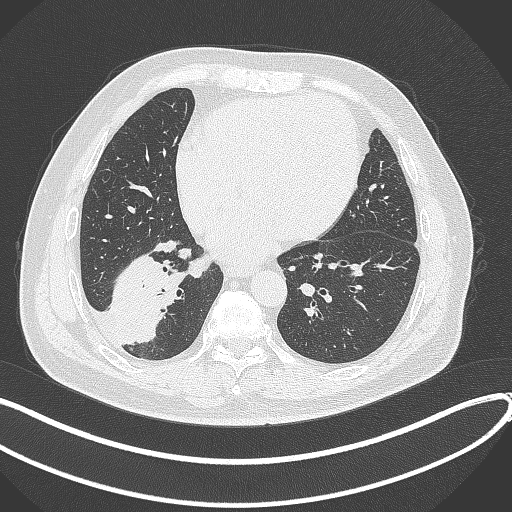
Chest CT, one axial slice. Position 129 of 360 along the scan axis. Lung window (W 1500 / L -600 HU). 1 mm slice thickness. 512 × 512 image matrix. Male patient, age 59 years.
Structures marked on this image (rectangle marked by the reading radiologist):
- lung tumour (recorded histology: adenocarcinoma): bounding box [x1, y1, x2, y2] px = [105, 248, 187, 348]